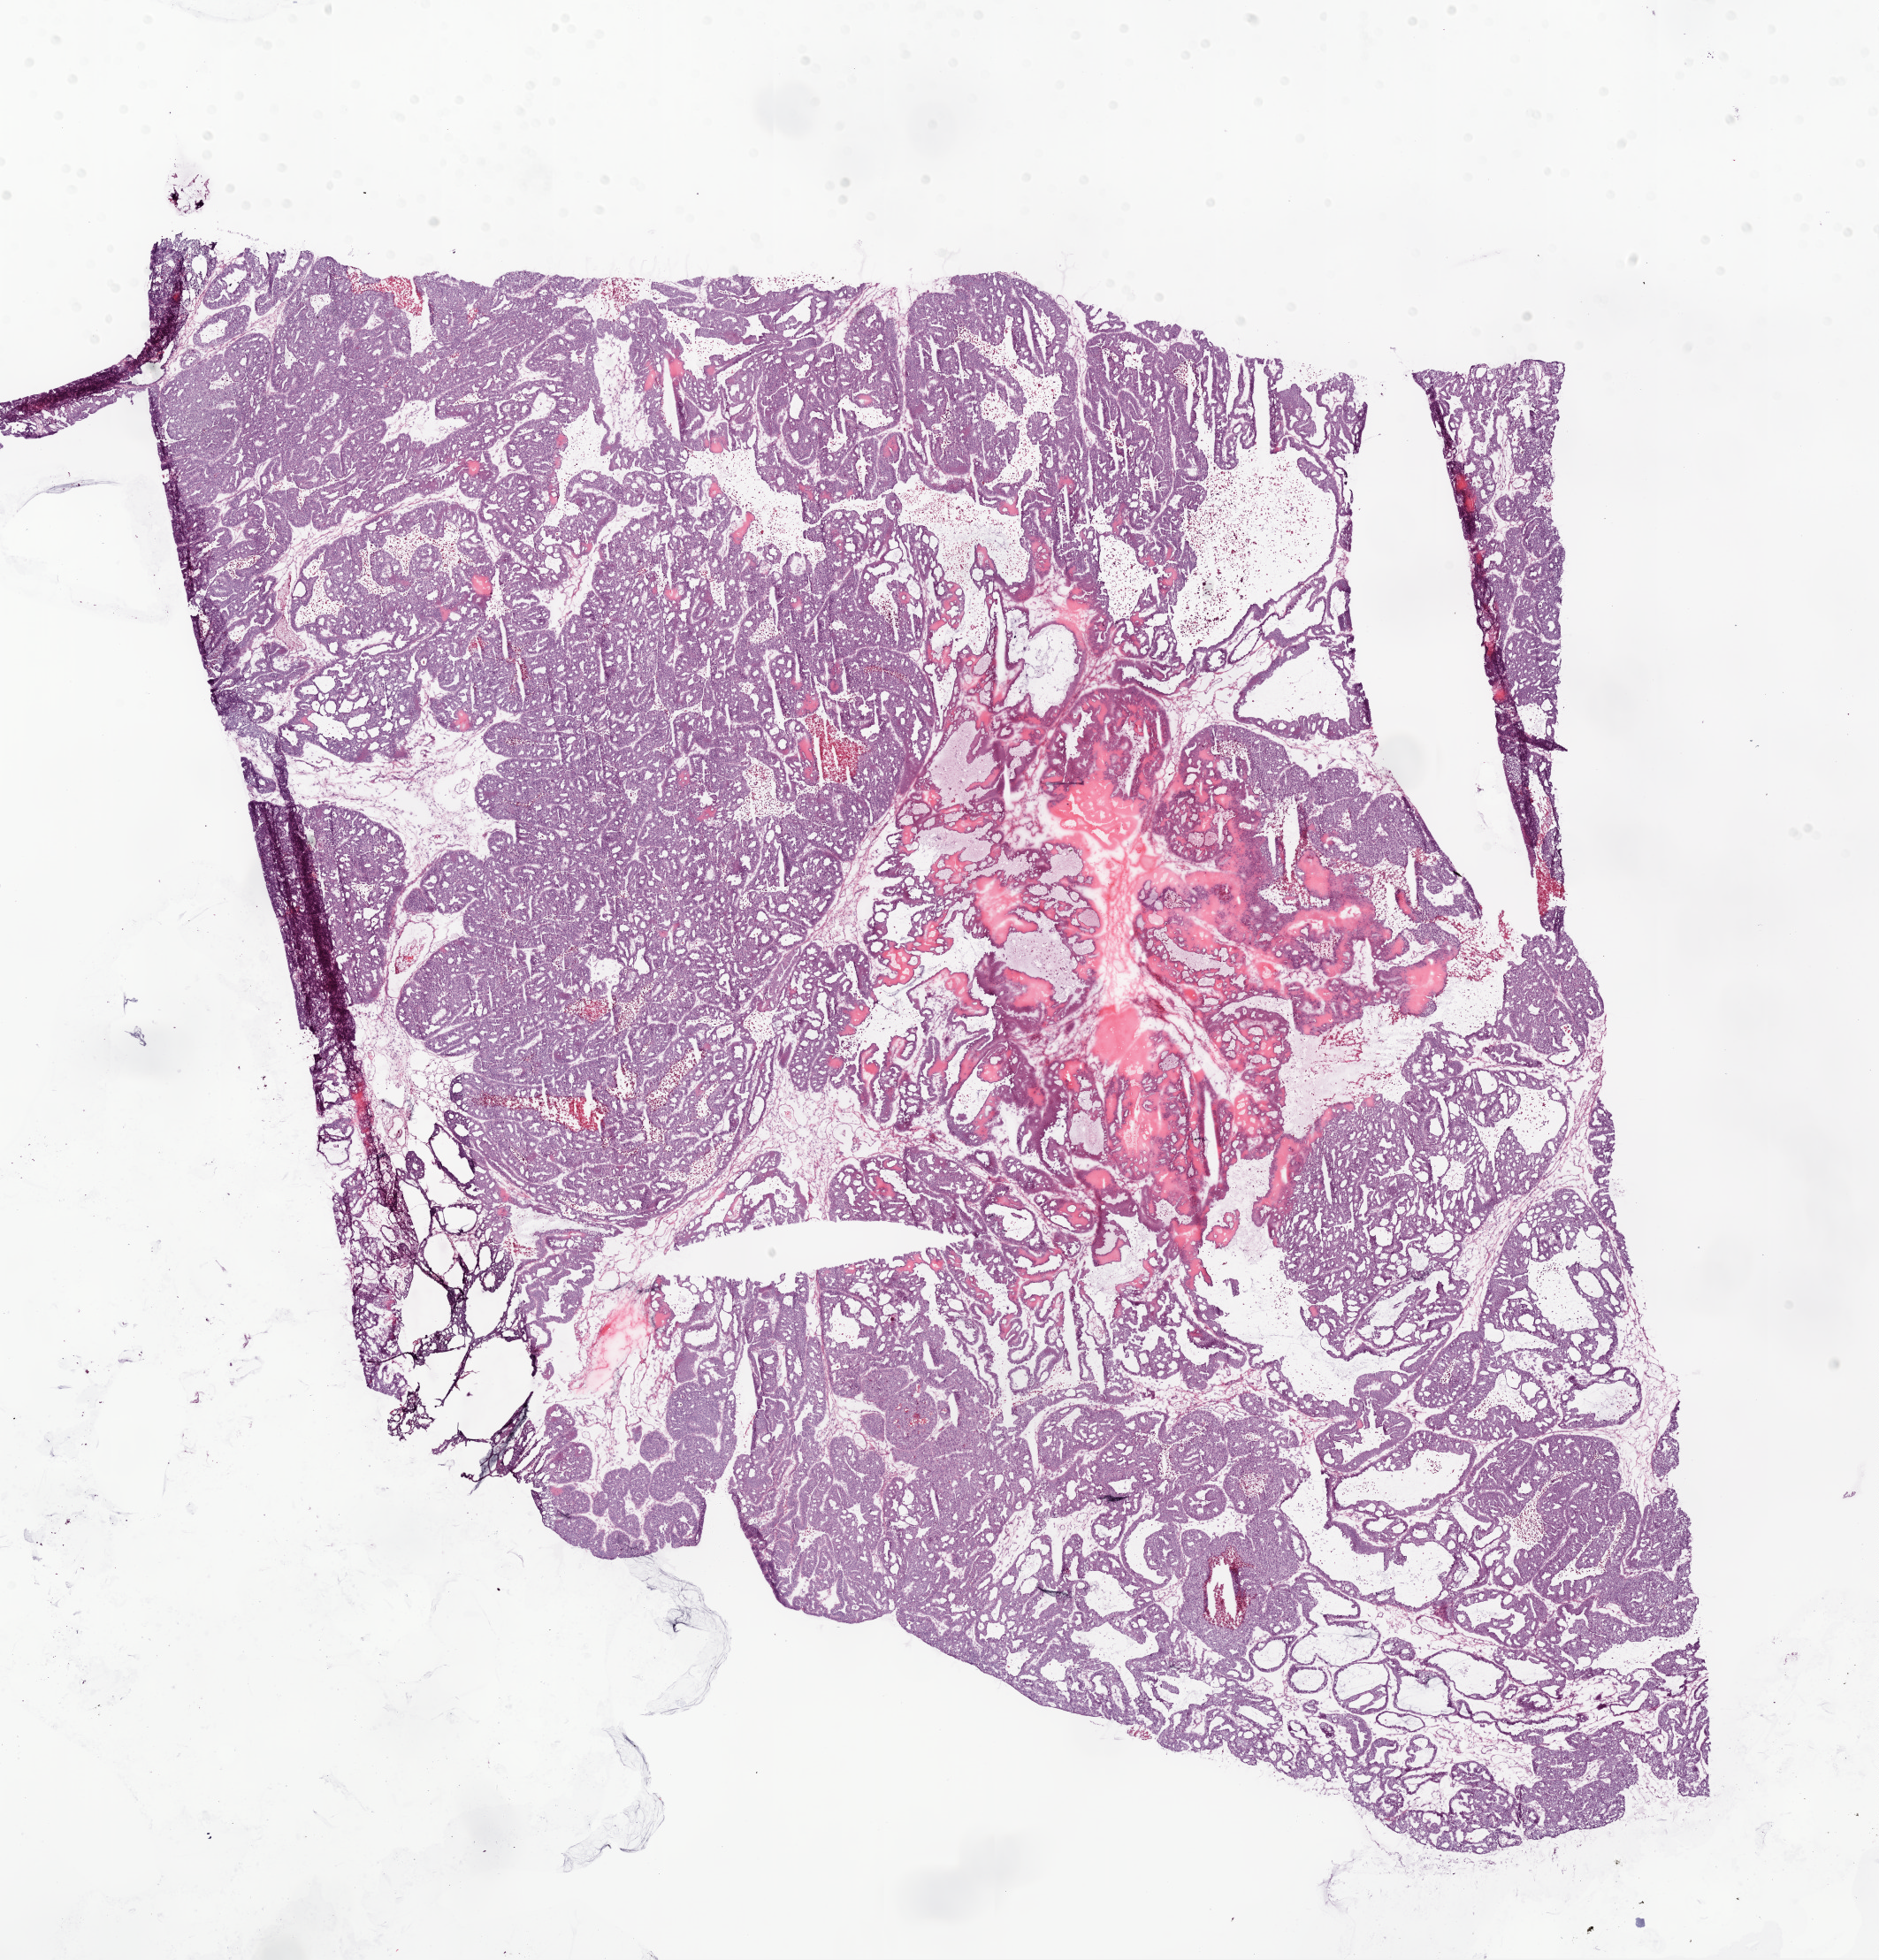
Whole-slide histology image, H&E — shown as a low-resolution overview of the whole scanned area (about 17.1 x 17.8 mm, slide scanned at 20x), frozen section from the bottom of the tissue portion, ovary, primary tumour sample. Female patient; age at initial diagnosis 57 years. Histologic grade: G3 (poorly differentiated). Pathologist review of this section (percent, as recorded): tumour cells 95%, tumour nuclei 99%, normal cells 0%, stromal cells 5%, necrosis 0%.
• FIGO stage: IIIC
• histologic diagnosis: Serous cystadenocarcinoma, NOS